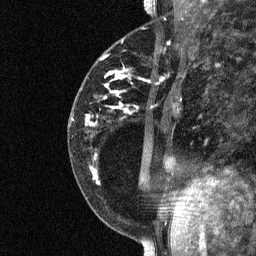
Breast MRI (dynamic contrast-enhanced), one sagittal slice. Slice 24 of 64 in the series (ordered by position). Dynamic contrast-enhanced study with each time point stored as its own series, time point 2 of 3 at this slice position (early post-contrast, ordered by acquisition time). 1.5 T. TE 4.8 ms, TR 27 ms. 2 mm slice thickness. 256 × 256 image matrix, field of view 180 × 180 mm. Patient: female, 34 years. Case-level facts recorded for this patient, not image findings: setting: breast cancer imaged before/during neoadjuvant chemotherapy; receptor status: HR-positive, HER2-negative.
Structures marked on this image (semi-automatic segmentation, software-assisted and operator-edited):
- analysis volume of interest (the breast-tissue region the enhancement analysis was run in; not a lesion): bounding box [x1, y1, x2, y2] px = [78, 44, 181, 191]
- tumour enhancement mask (voxels above the 90 % enhancement threshold inside the analysis volume of interest): [88, 74, 123, 183]